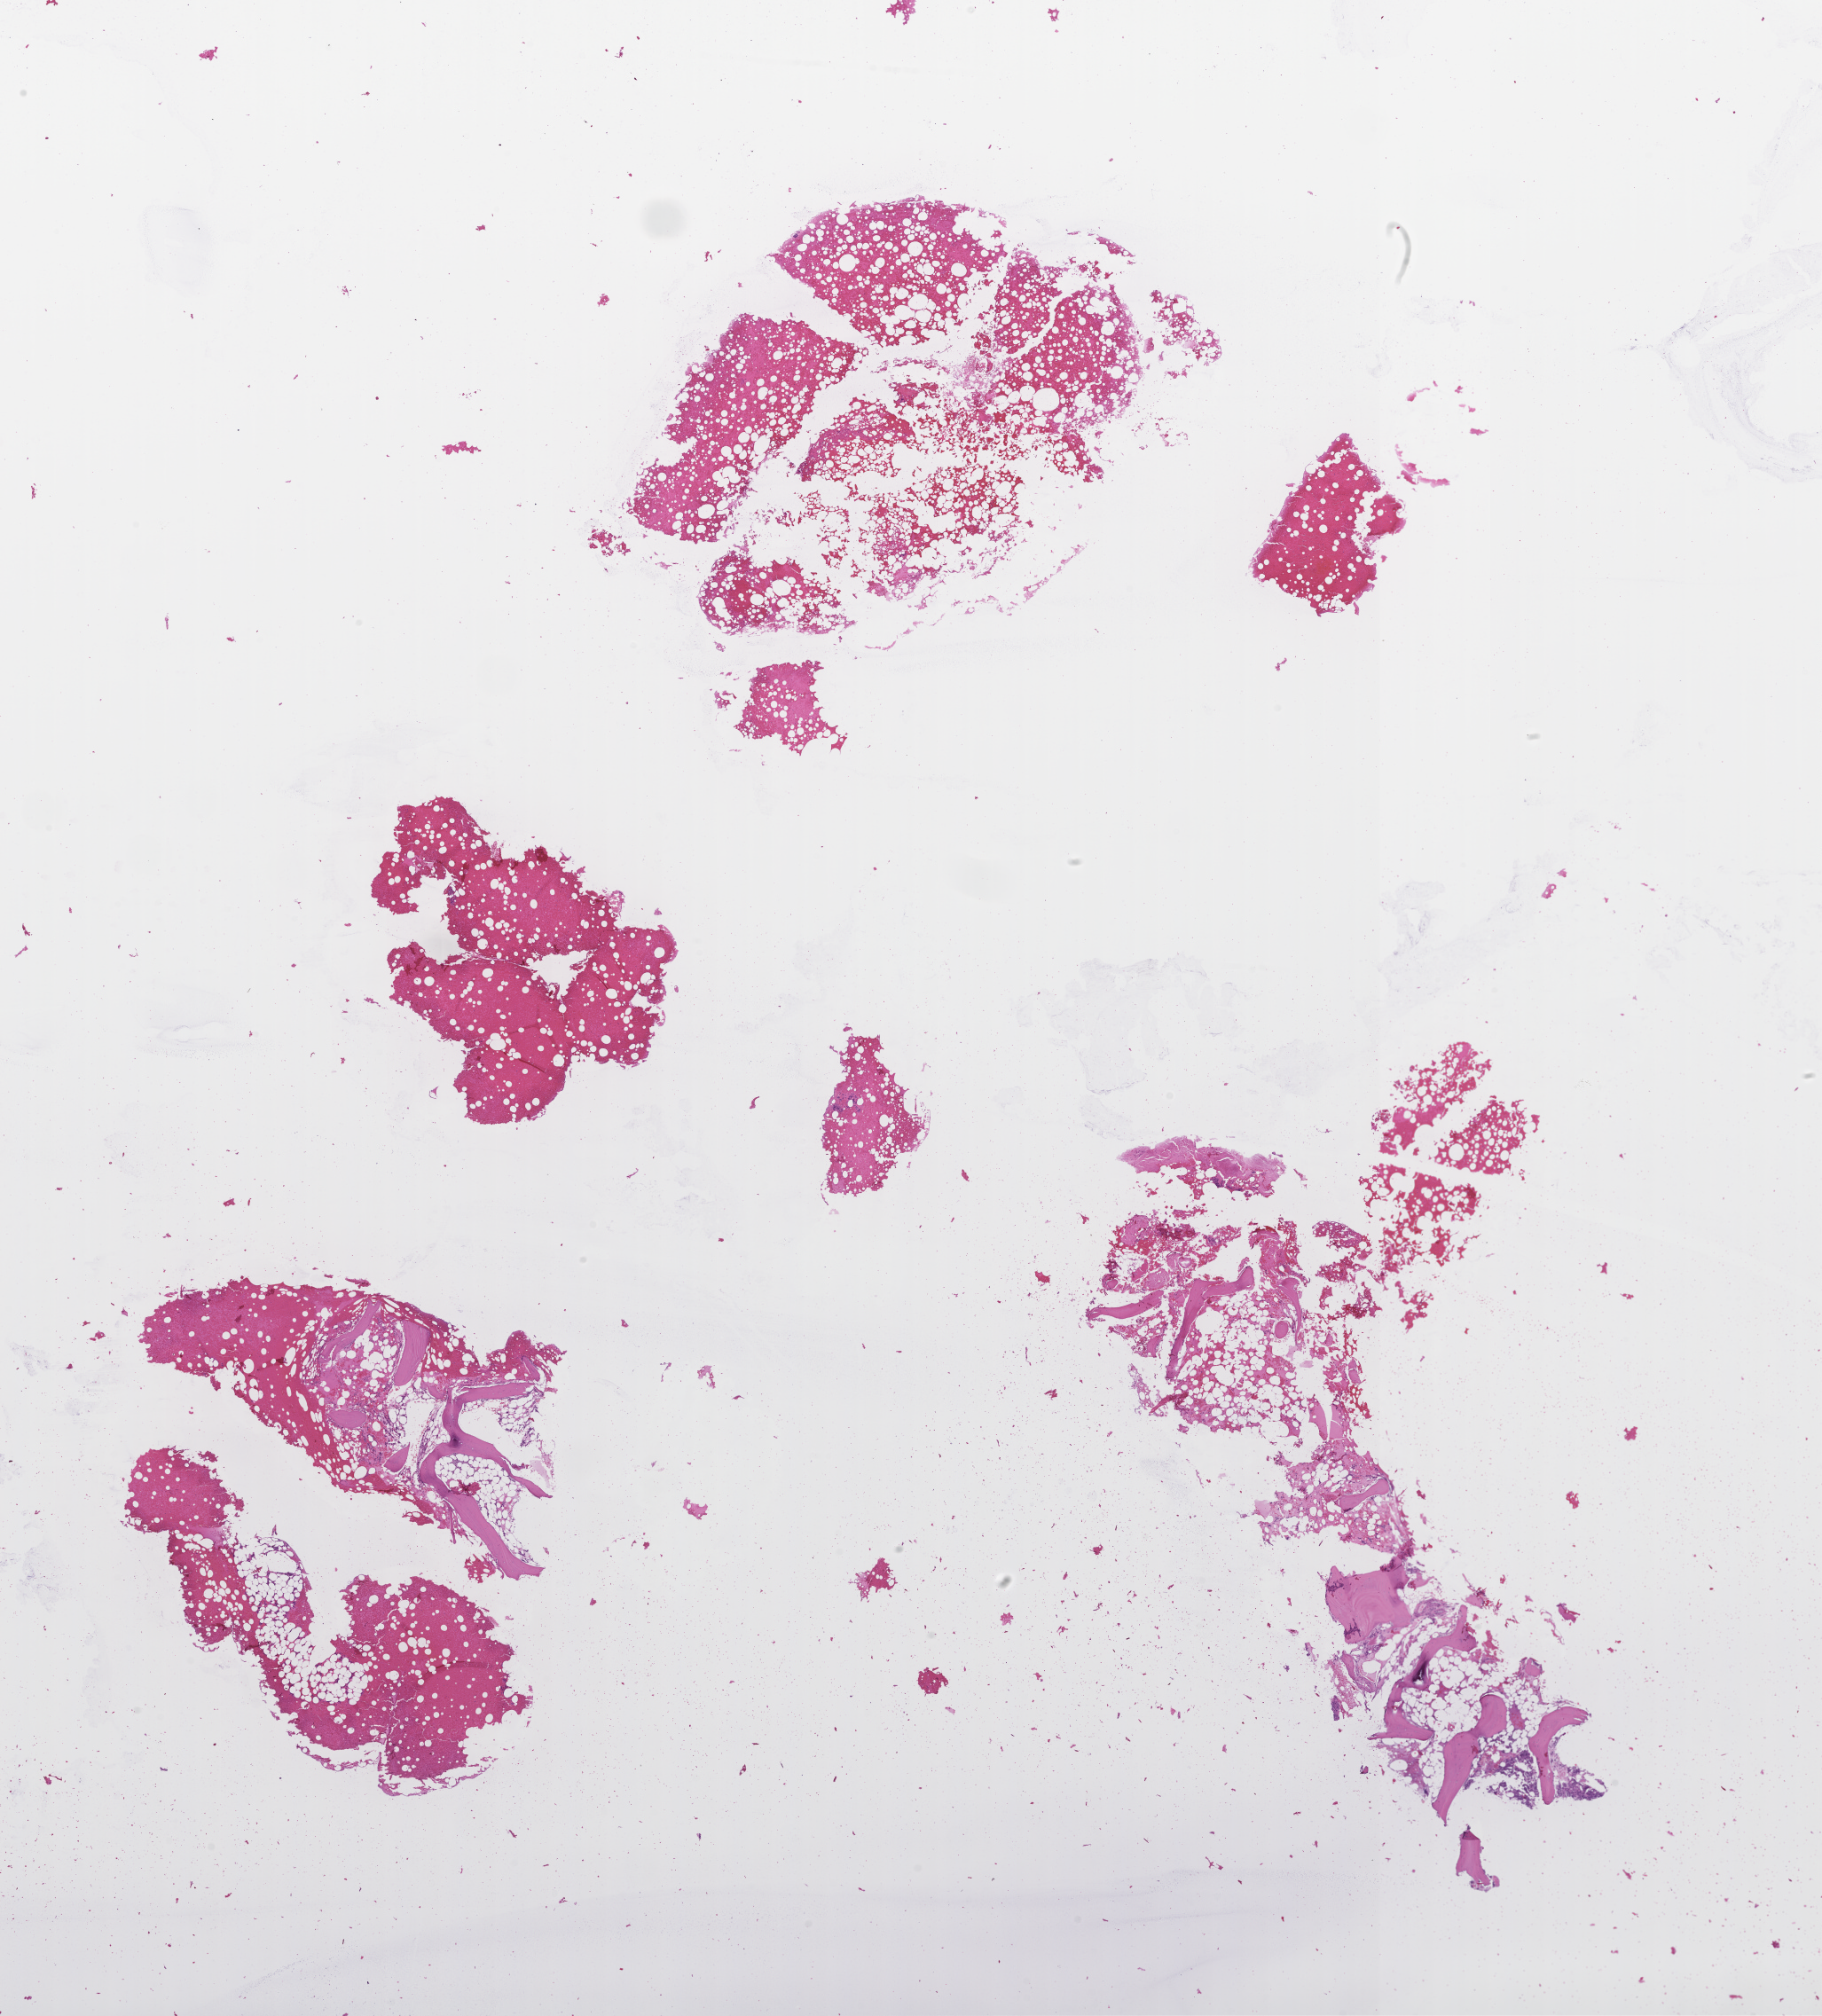
Haematoxylin and eosin whole-slide image, a low-resolution overview of the entire scanned area, about 16.6 x 18.4 mm. FFPE section. Site: bone marrow. Archival tissue. Patient sex: male.
This section: primary tumour tissue. Diagnosis: Plasma Cell Myeloma.